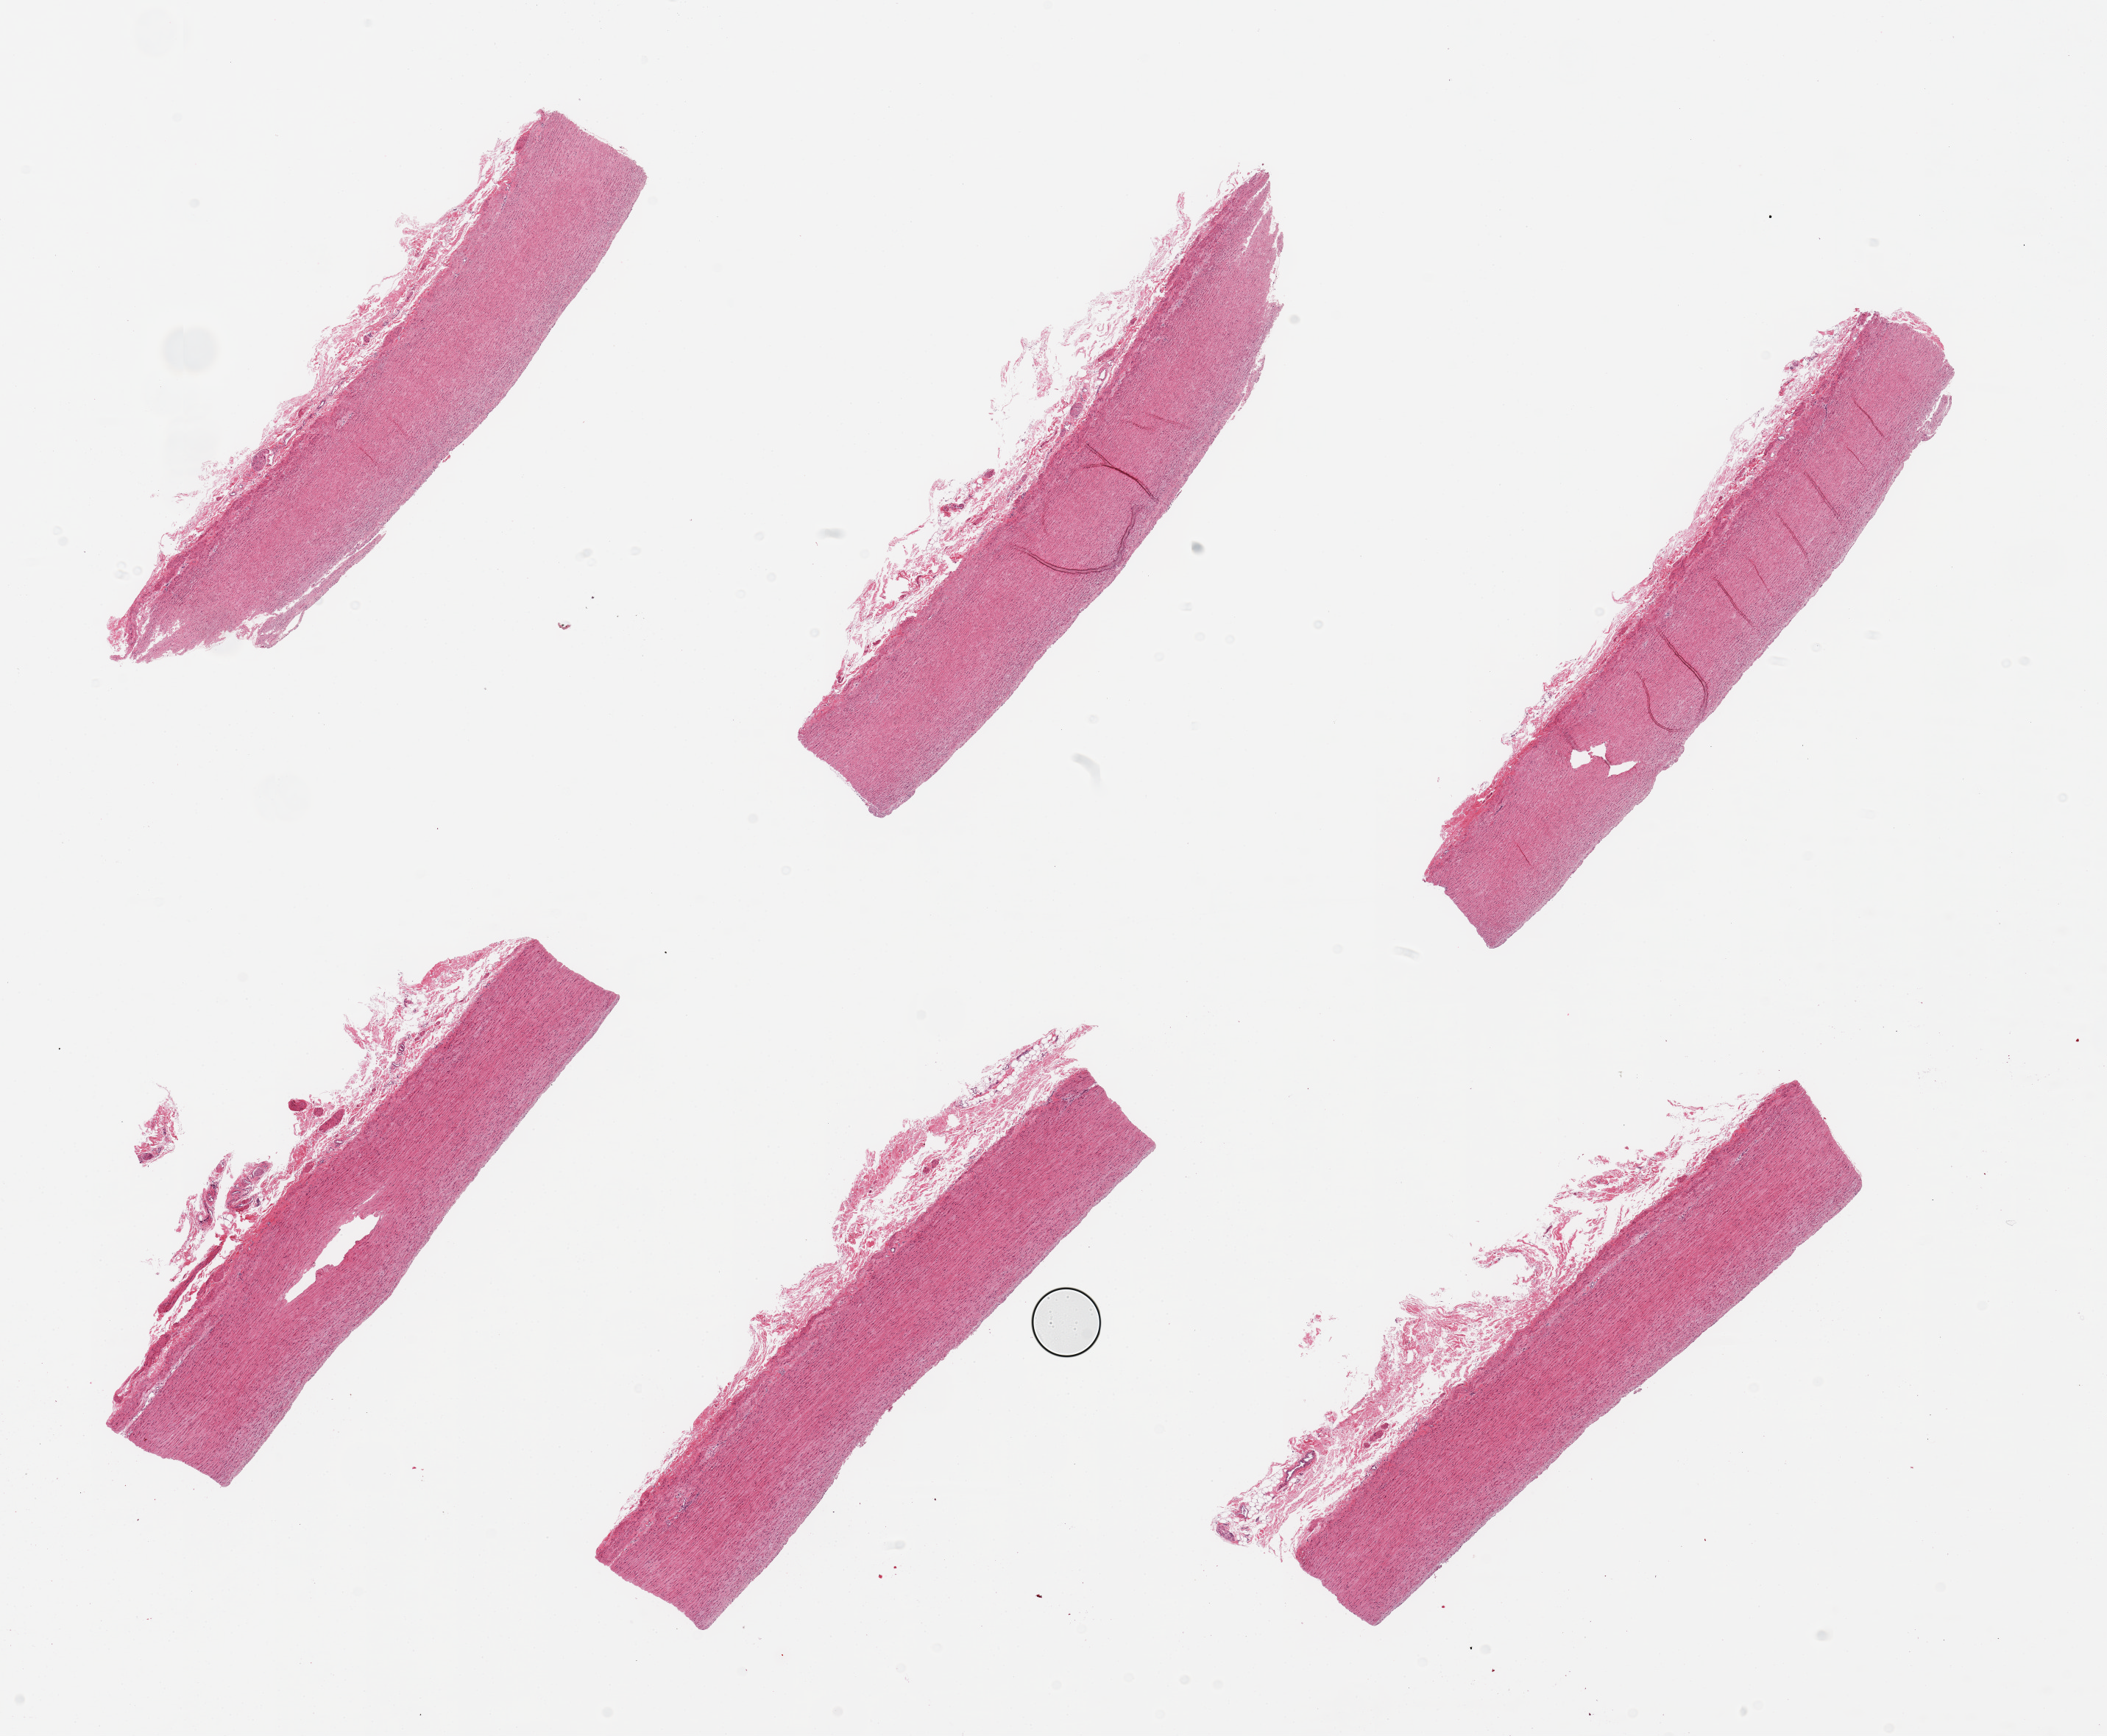
H&E whole-slide image, whole scanned area (about 22.6 x 18.7 mm) shown as a low-resolution overview. PAXgene-fixed paraffin-embedded (PFPE) section. Sampled site (target tissue): aorta. Donor tissue sample. Donor sex: female.
Pathologist's review note for this sample: 6 pieces; no plaques; well trimmed.